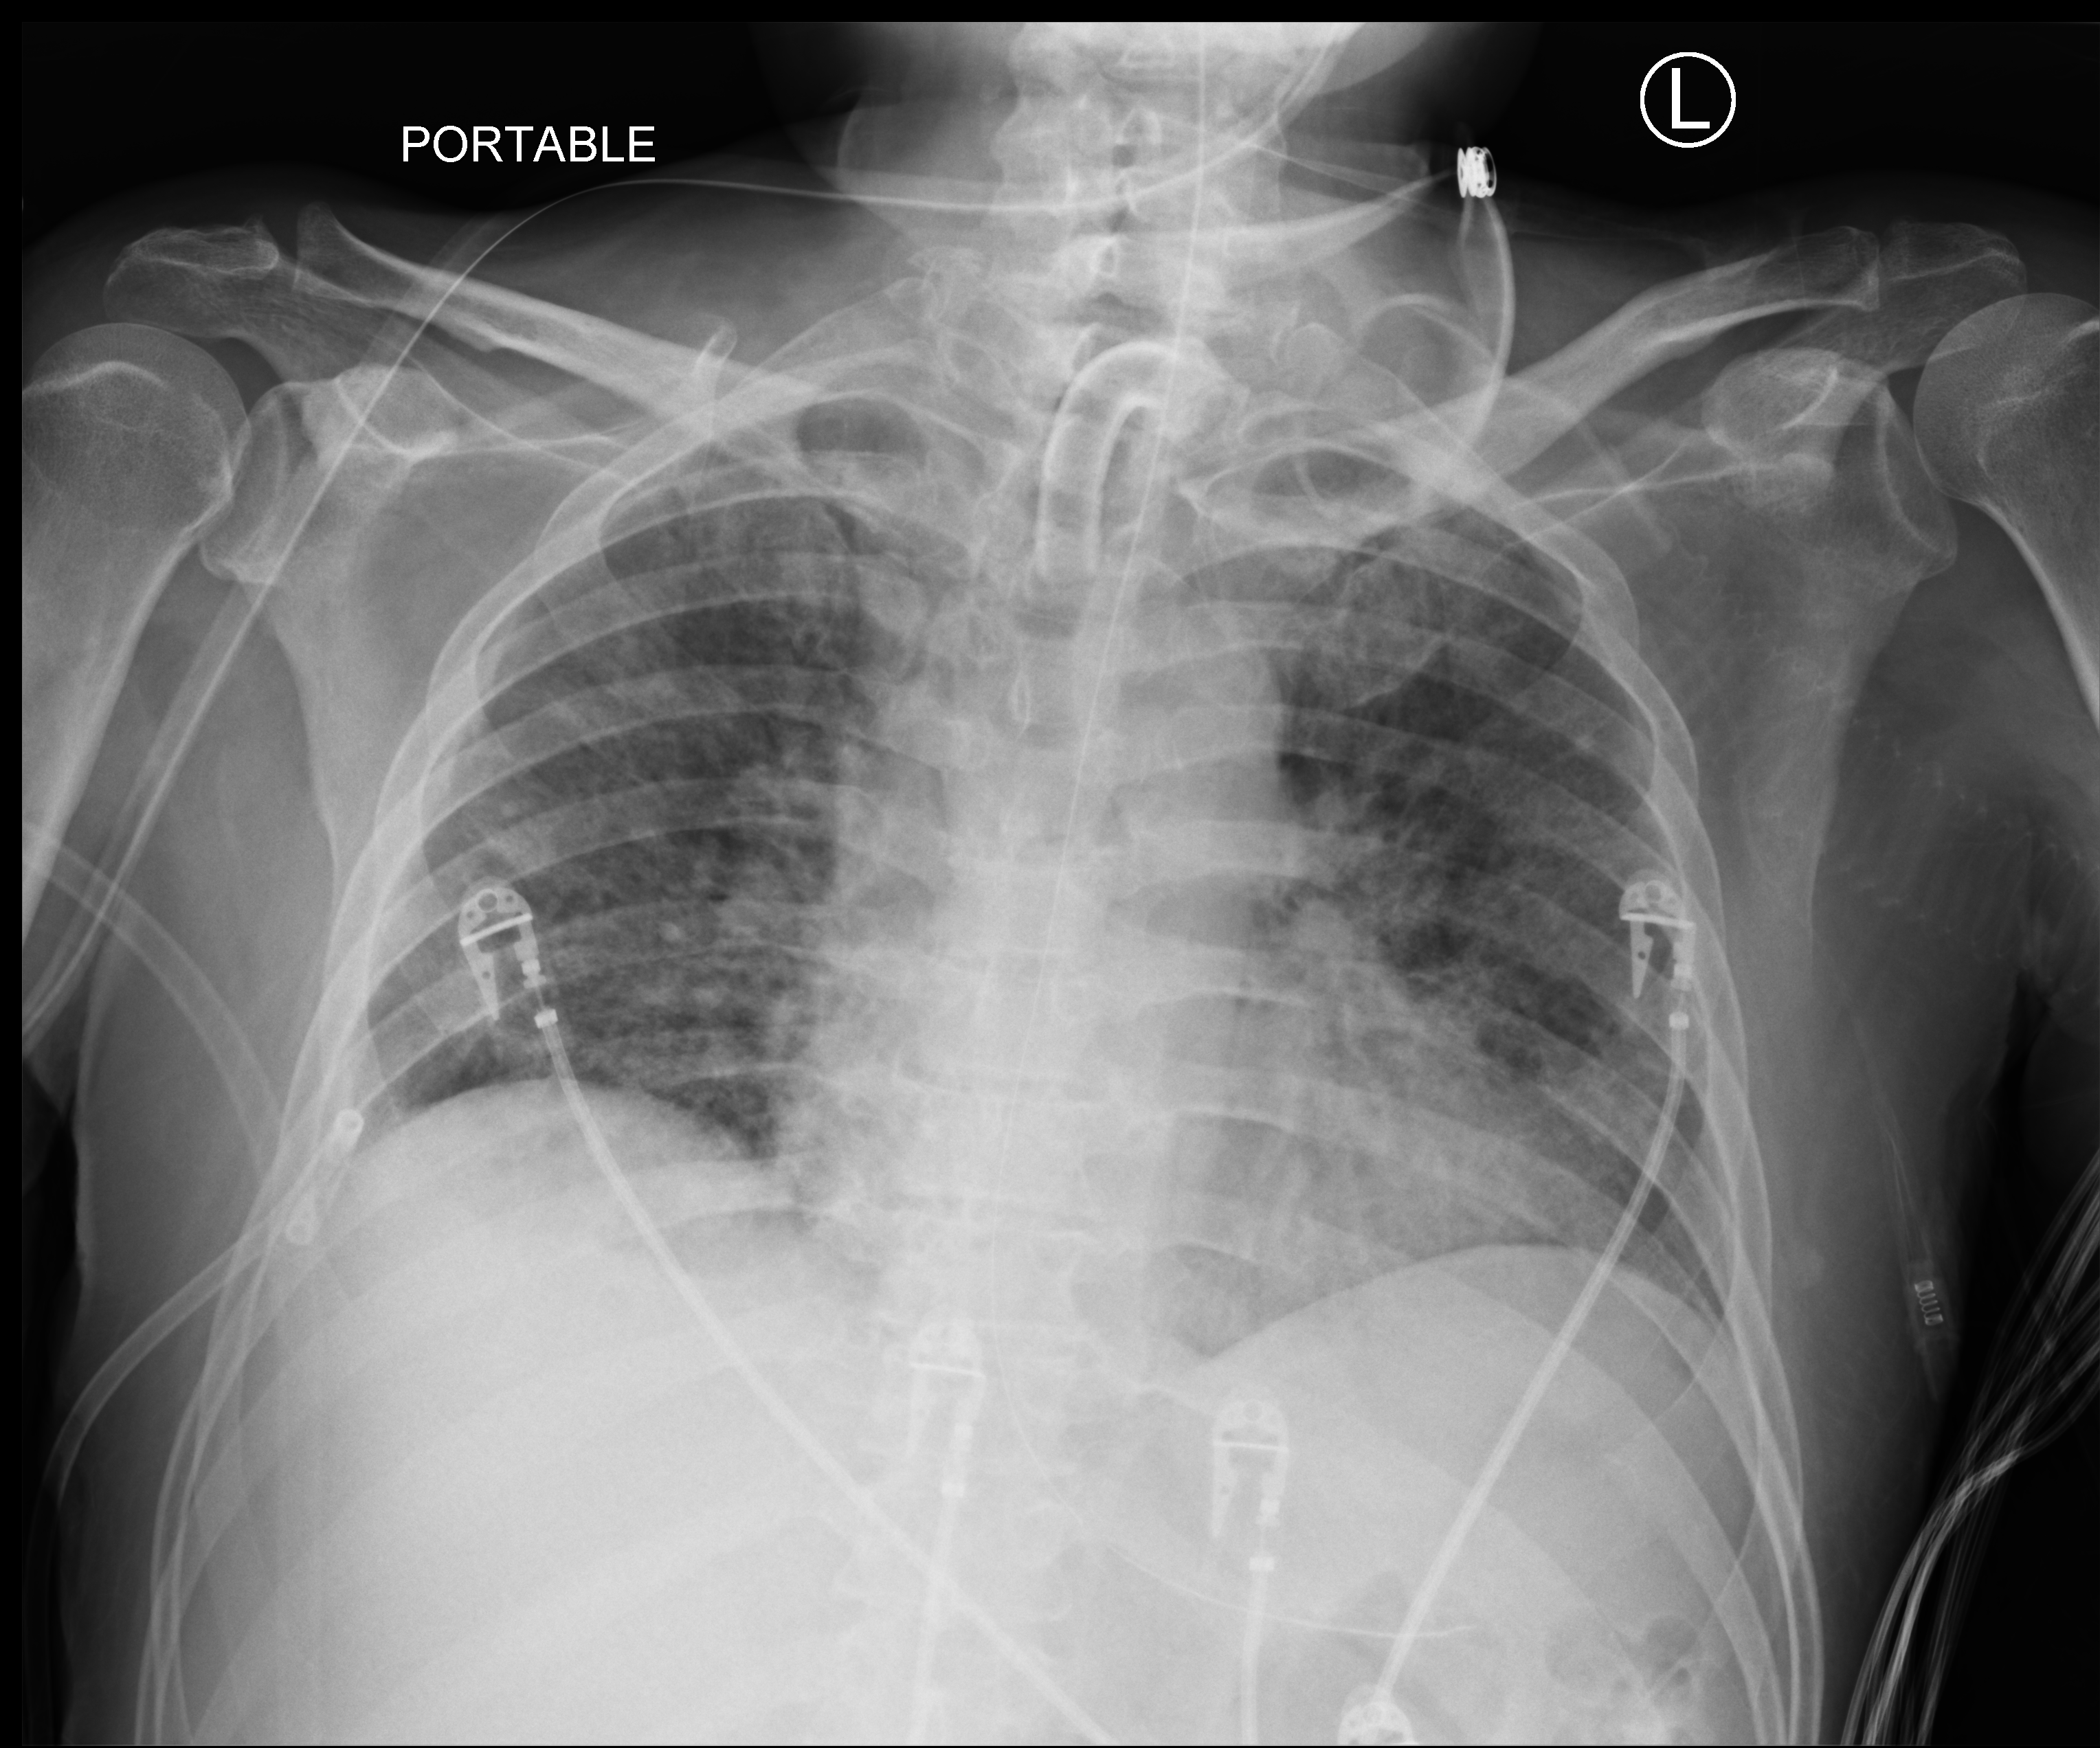
Portable chest radiograph. Patient hospitalised with COVID-19; male, aged 18–59 years.
From the hospital-stay record, not from the radiograph (when in the stay this image was taken is not recorded):
- diabetes (admission record): no